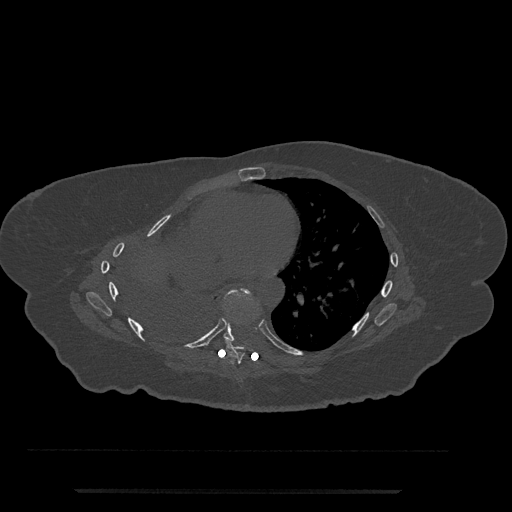
CT including the spine, one axial slice; position 420 of 797 along the scan axis; 120 kVp; bone window (W 1800 / L 400 HU); 512 × 512 image matrix, field of view 440 × 440 mm. Female patient, age 51 years. Case-level facts recorded for this patient, not image findings: primary cancer: neuro.
Annotated regions visible in this slice (semi-automatic segmentation, software-assisted and operator-edited):
- T7 vertebra: box from (x=223, y=340) to (x=245, y=364) px
- T8 vertebra: (x=223, y=288)–(x=250, y=342)